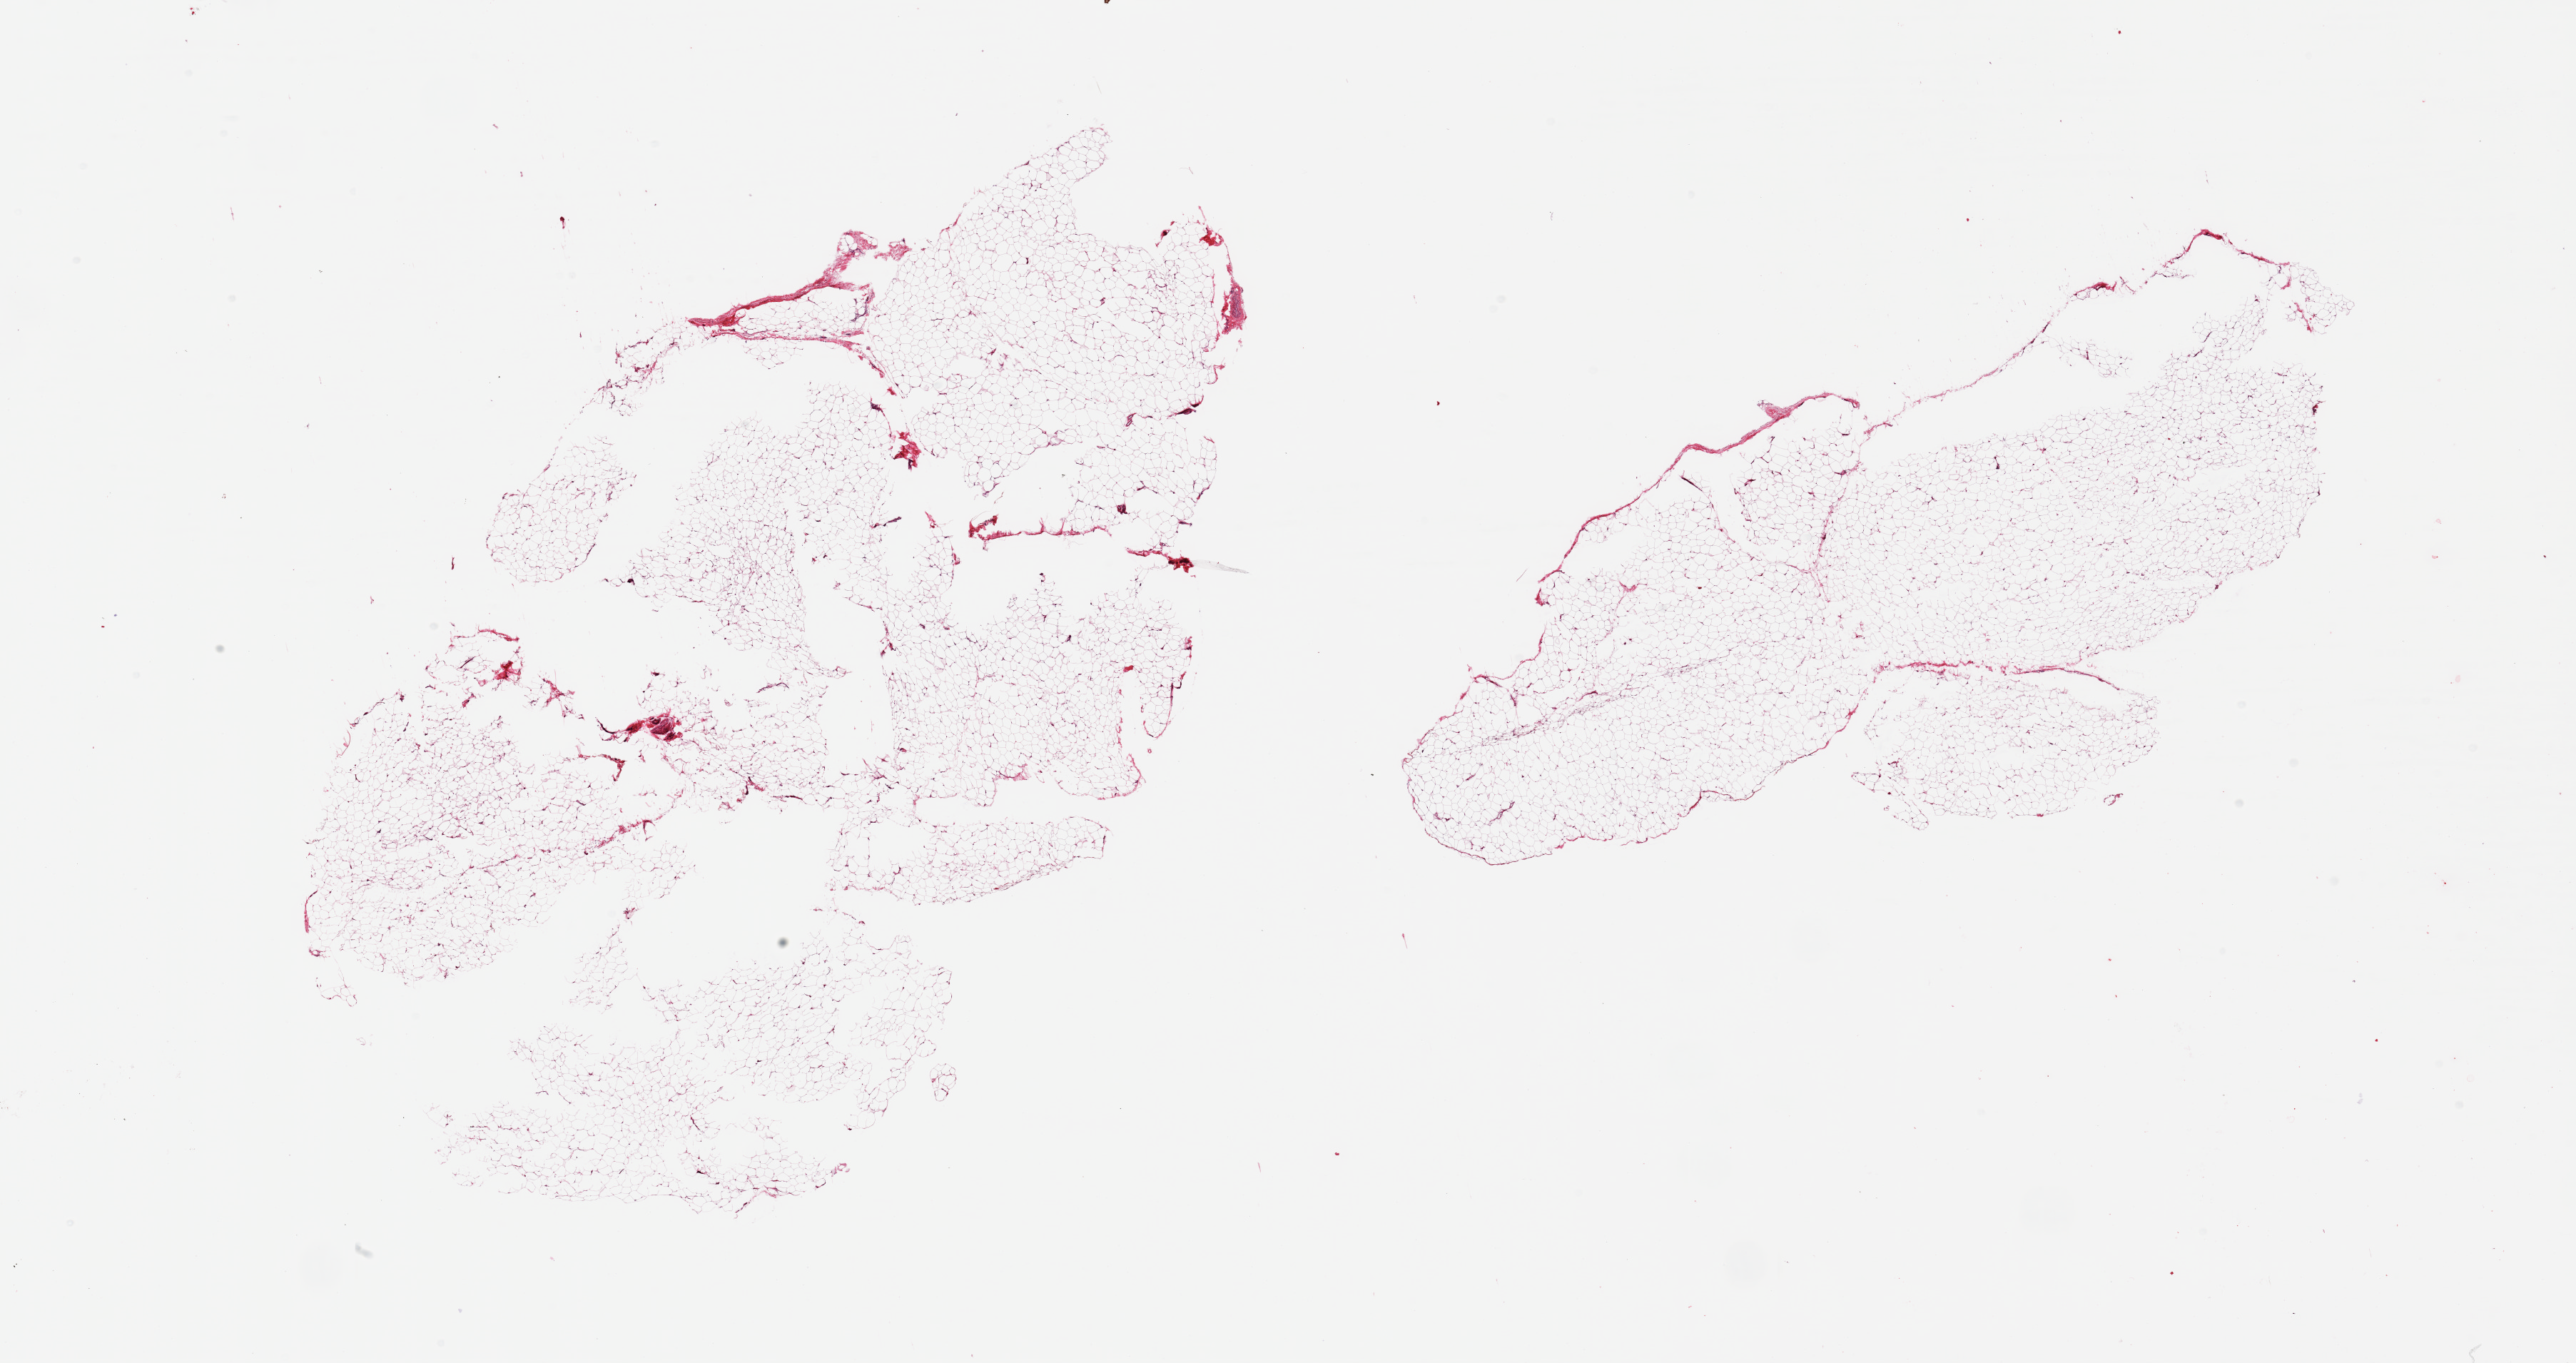
Whole-slide image, H&E stain — low-resolution overview of the scanned area, about 28.5 x 15.1 mm; PAXgene-fixed paraffin-embedded (PFPE) section; section of adipose tissue (target tissue); donor tissue sample. Donor sex: female.
Review note (as recorded): 2 pieces; mature adipose tissue, few holes (? poor fixation).